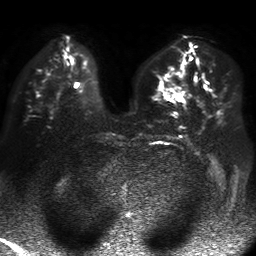
Breast MRI, one axial slice. Position 24 of 50 along the scan axis. Diffusion-weighted series; image 2 of 4 stored at this slice position (different b-values; order by instance number). 1.5 T. 256 × 256 image matrix. Female patient.
Outlined on this slice (outlined manually by an expert reader):
- tumour on diffusion-weighted imaging: bounding box [x1, y1, x2, y2] px = [176, 95, 184, 101]